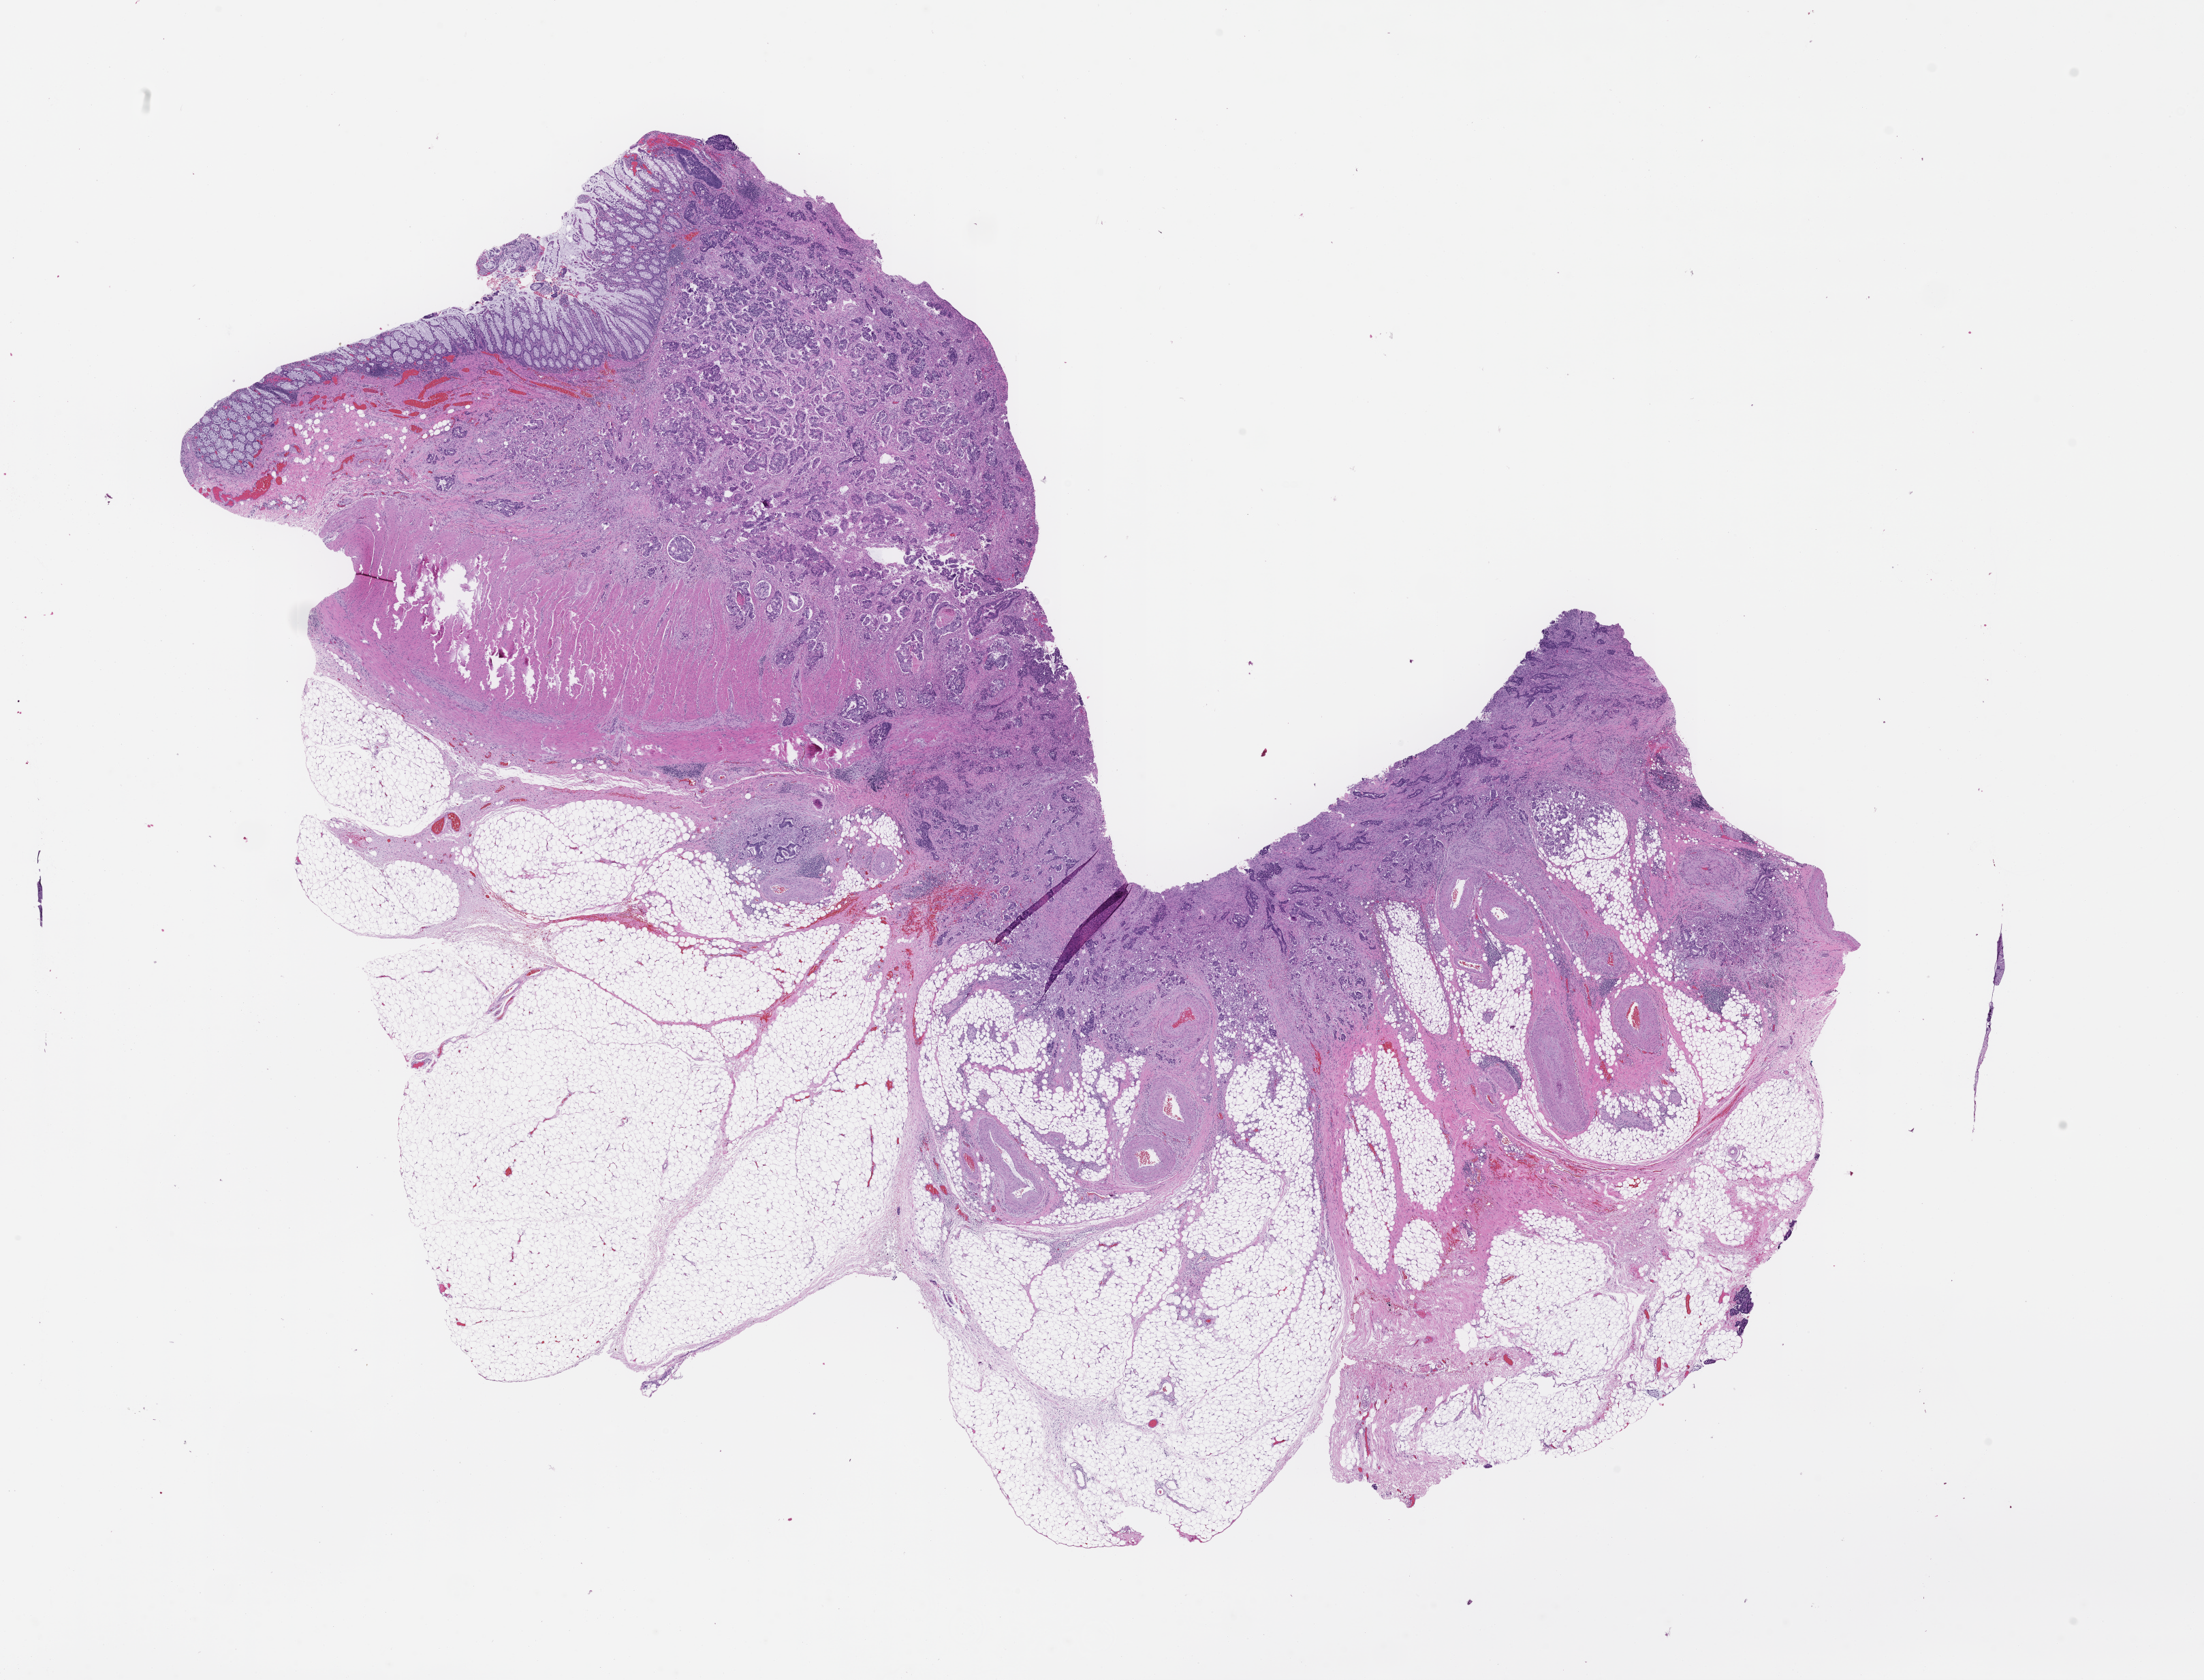
Digitized H&E-stained section — shown as a low-resolution overview of the whole scanned area (about 26.1 x 19.9 mm); formalin-fixed paraffin-embedded section; tissue site: colon. Female patient.
This section: primary tumour tissue. Diagnosis: Colorectal Carcinoma.